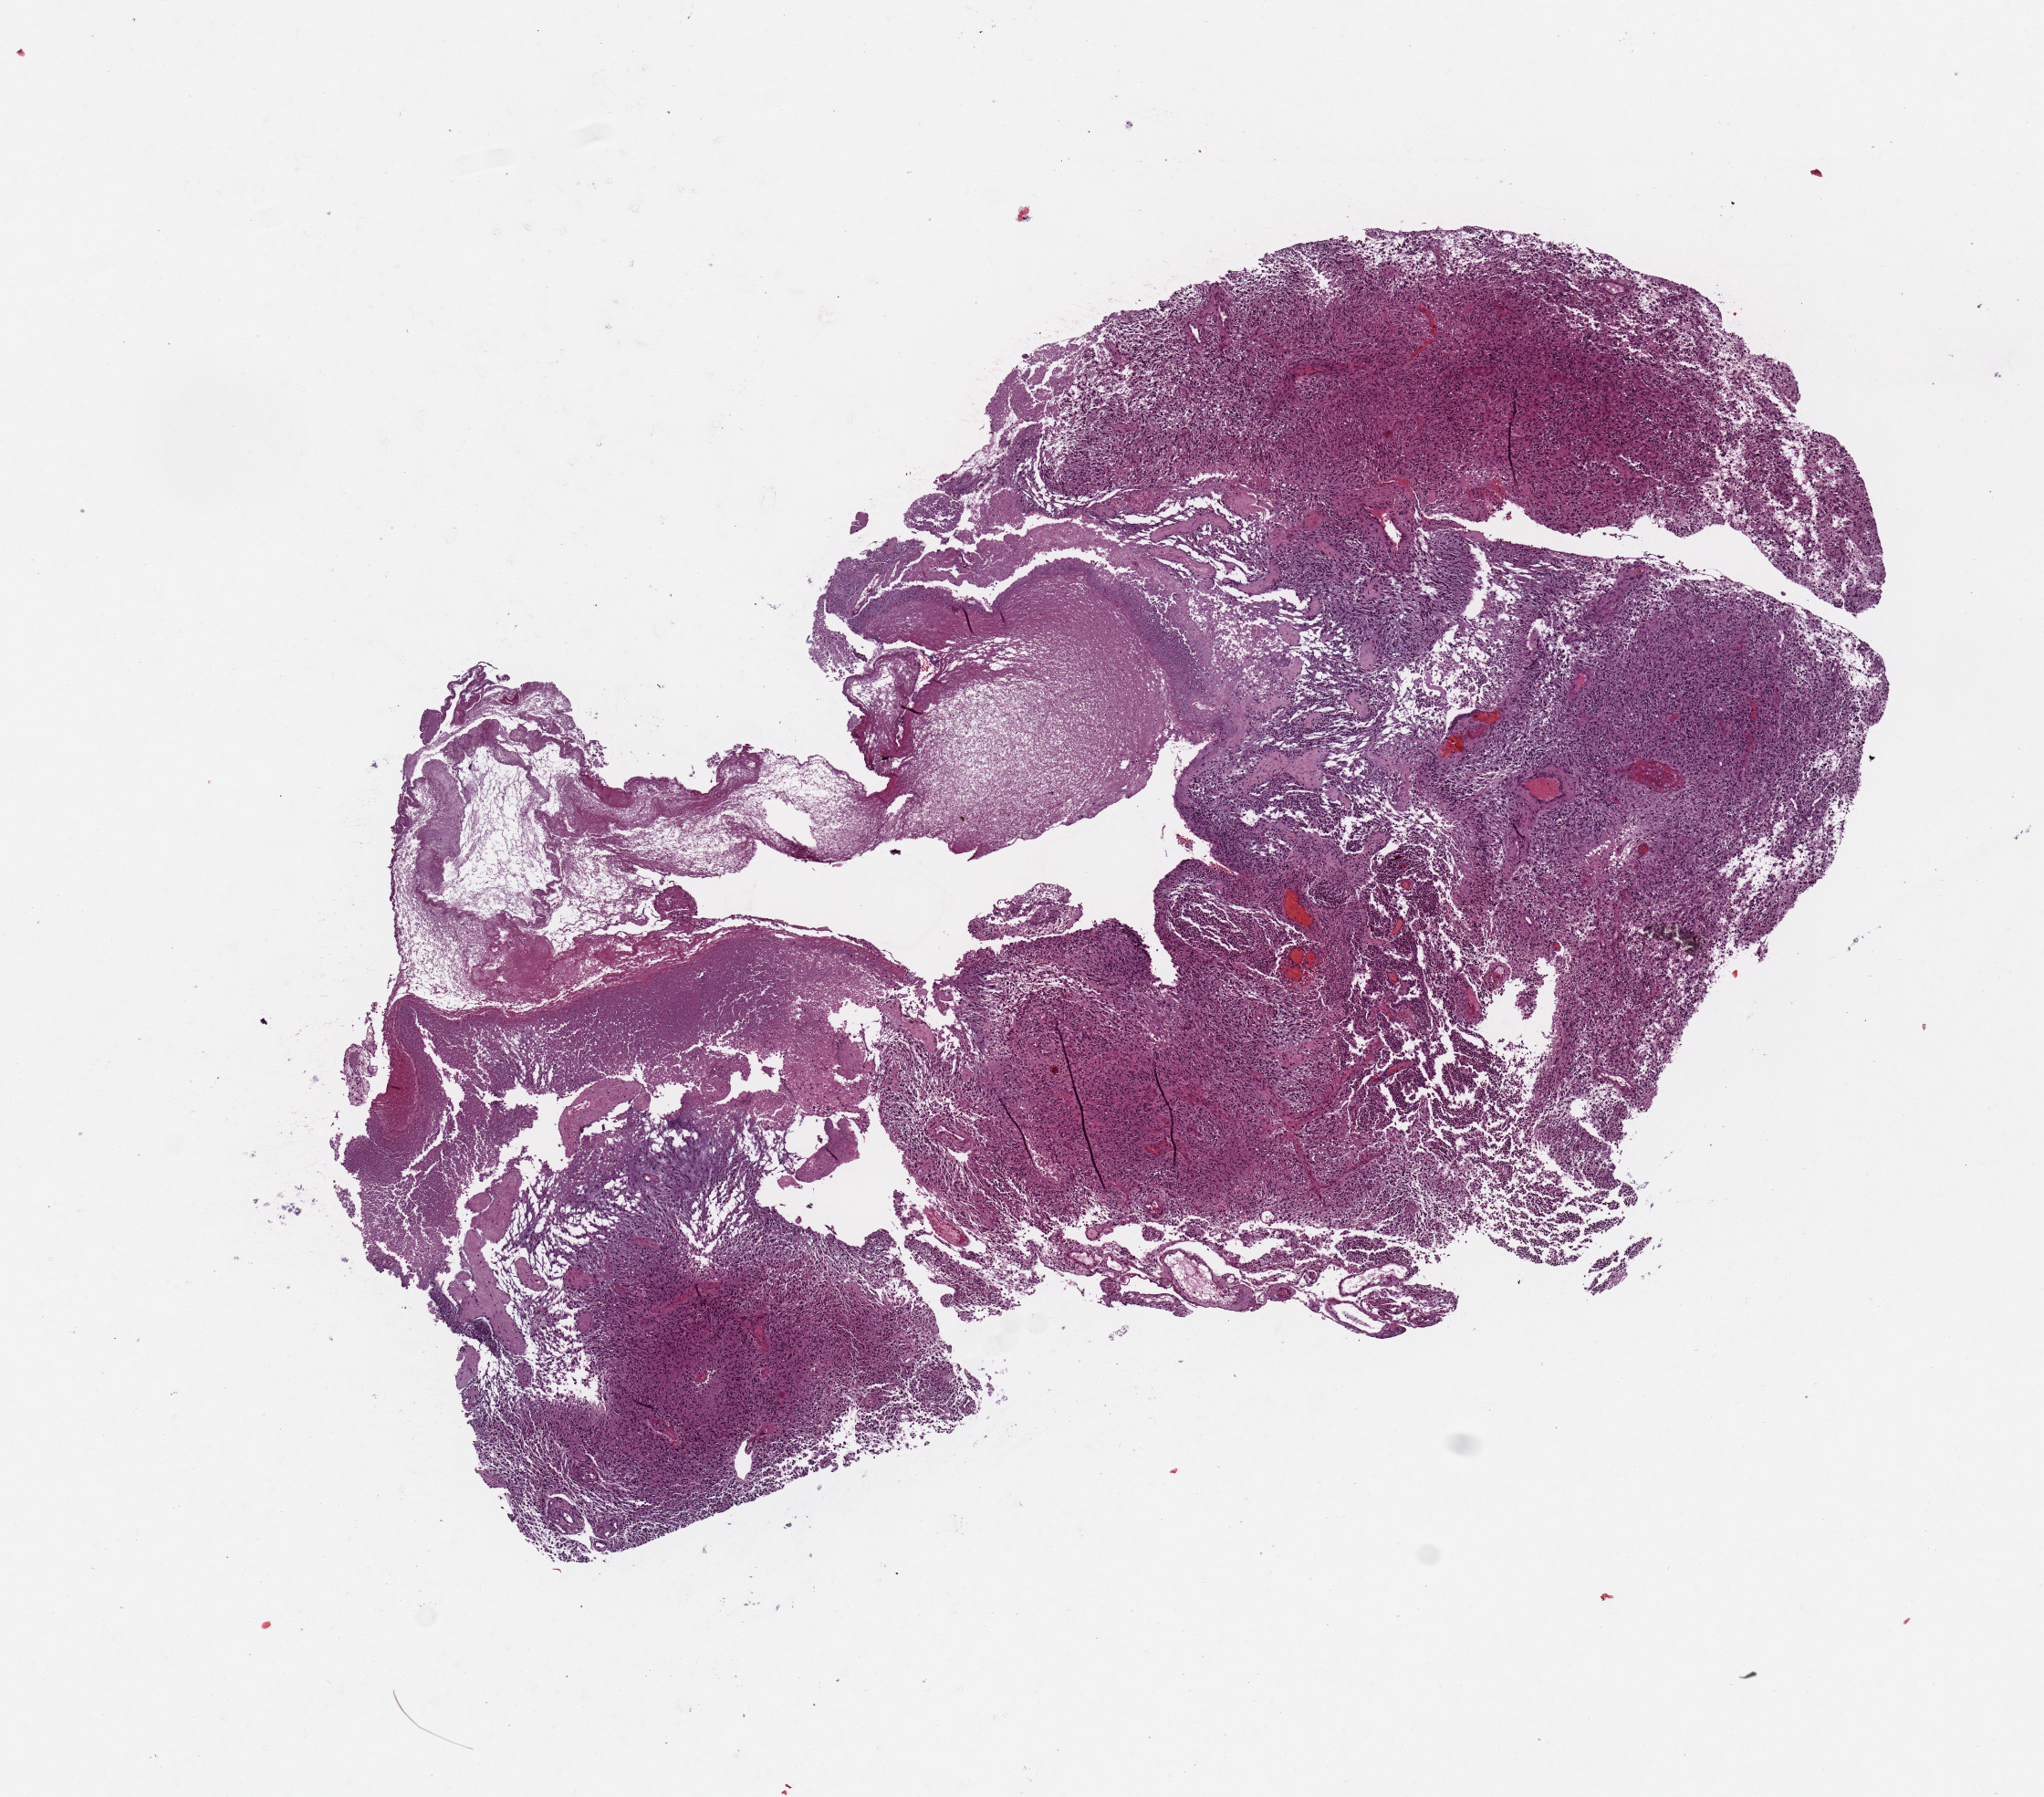
Whole-slide histology image, H&E-stained, low-resolution overview of the scanned area, about 8.9 x 7.8 mm; tumour tissue sample, brain. Female, 53 y/o.
Histologic diagnosis: Glioblastoma. Primary tumour site (as recorded): temporal lobe.